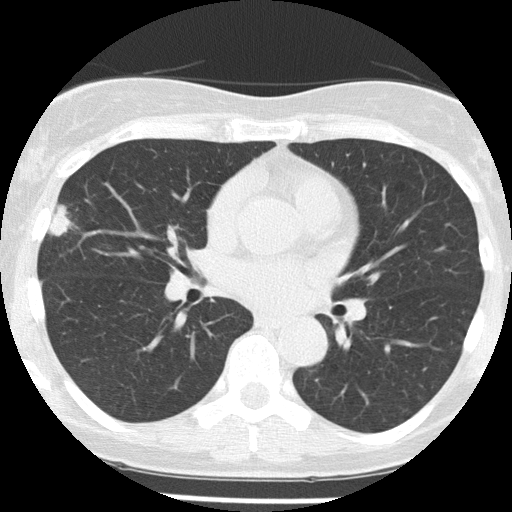
Chest CT (low-dose screening protocol), one axial image. Baseline screening round. Lung window (W 1500 / L -600 HU). 2 mm slice thickness. Lung (sharp) reconstruction kernel (FC51). Slice 73 of 156 in the series. Female, age 58 years at enrolment. Former smoker at enrolment.
Expert-annotated lung lesion, bounding box <29,195,88,255> (left, top, right, bottom; pixels). The exam's reader record, not a measurement of the box and not confirmed to be the same lesion: non-calcified nodule or mass ≥4 mm, right middle lobe, 18 × 9 mm, spiculated (stellate) margins, soft tissue attenuation. Lung cancer was diagnosed 79 days after this screen: non-small cell carcinoma, right middle lobe, poorly differentiated (G3), stage IA (AJCC 6th edition), 18 mm at pathology.